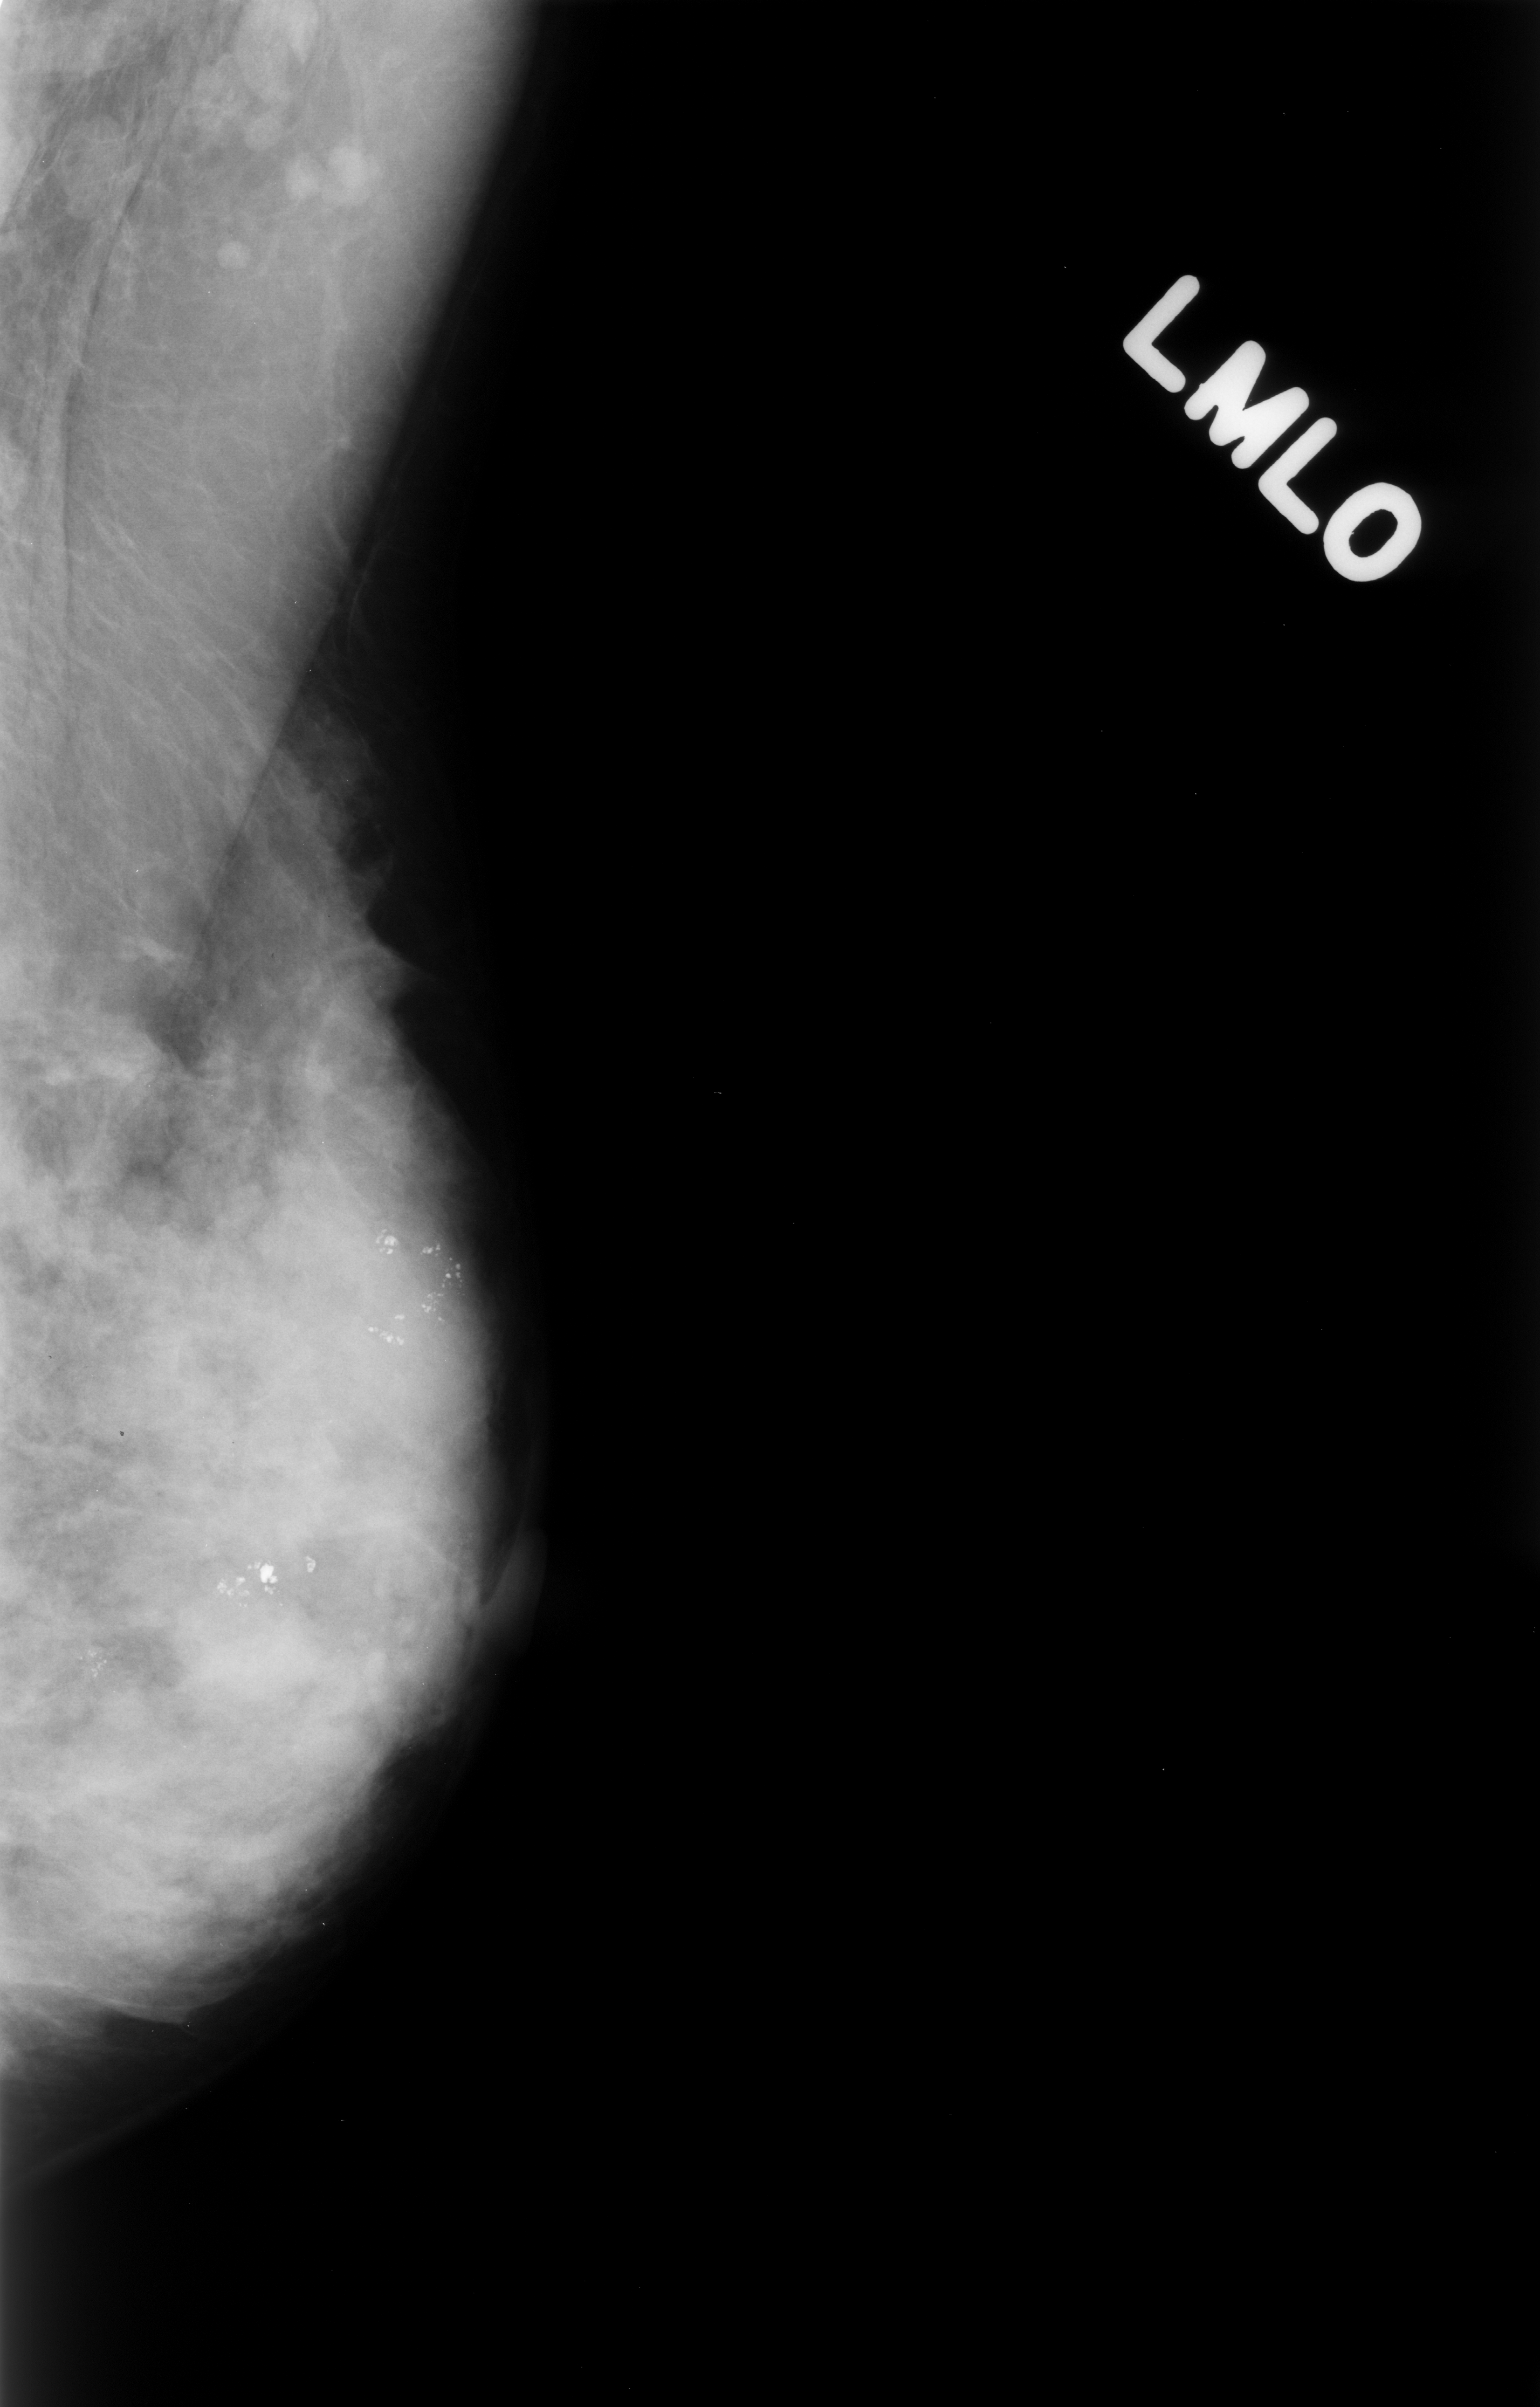
Mammogram (digitized film); left breast; MLO view; 1540 × 2407 image matrix.
Expert-marked regions of interest on this image (one box per marked abnormality):
- Finding 1 of 3: calcifications, morphology pleomorphic, distribution clustered; BI-RADS assessment category 4; subtlety rating 5 on a 1 (subtle) to 5 (obvious) scale; pathology result (as recorded, not read from the image): benign: bounding box <43,1613,156,1774> (left, top, right, bottom; pixels)
- Finding 2 of 3: calcifications, morphology pleomorphic, distribution clustered; BI-RADS assessment category 4; pathology (as recorded): benign: <189,1514,359,1653>
- Finding 3 of 3: calcifications, morphology pleomorphic, distribution clustered; BI-RADS assessment category 4; pathology result (as recorded, not read from the image): benign: <314,1181,510,1403>